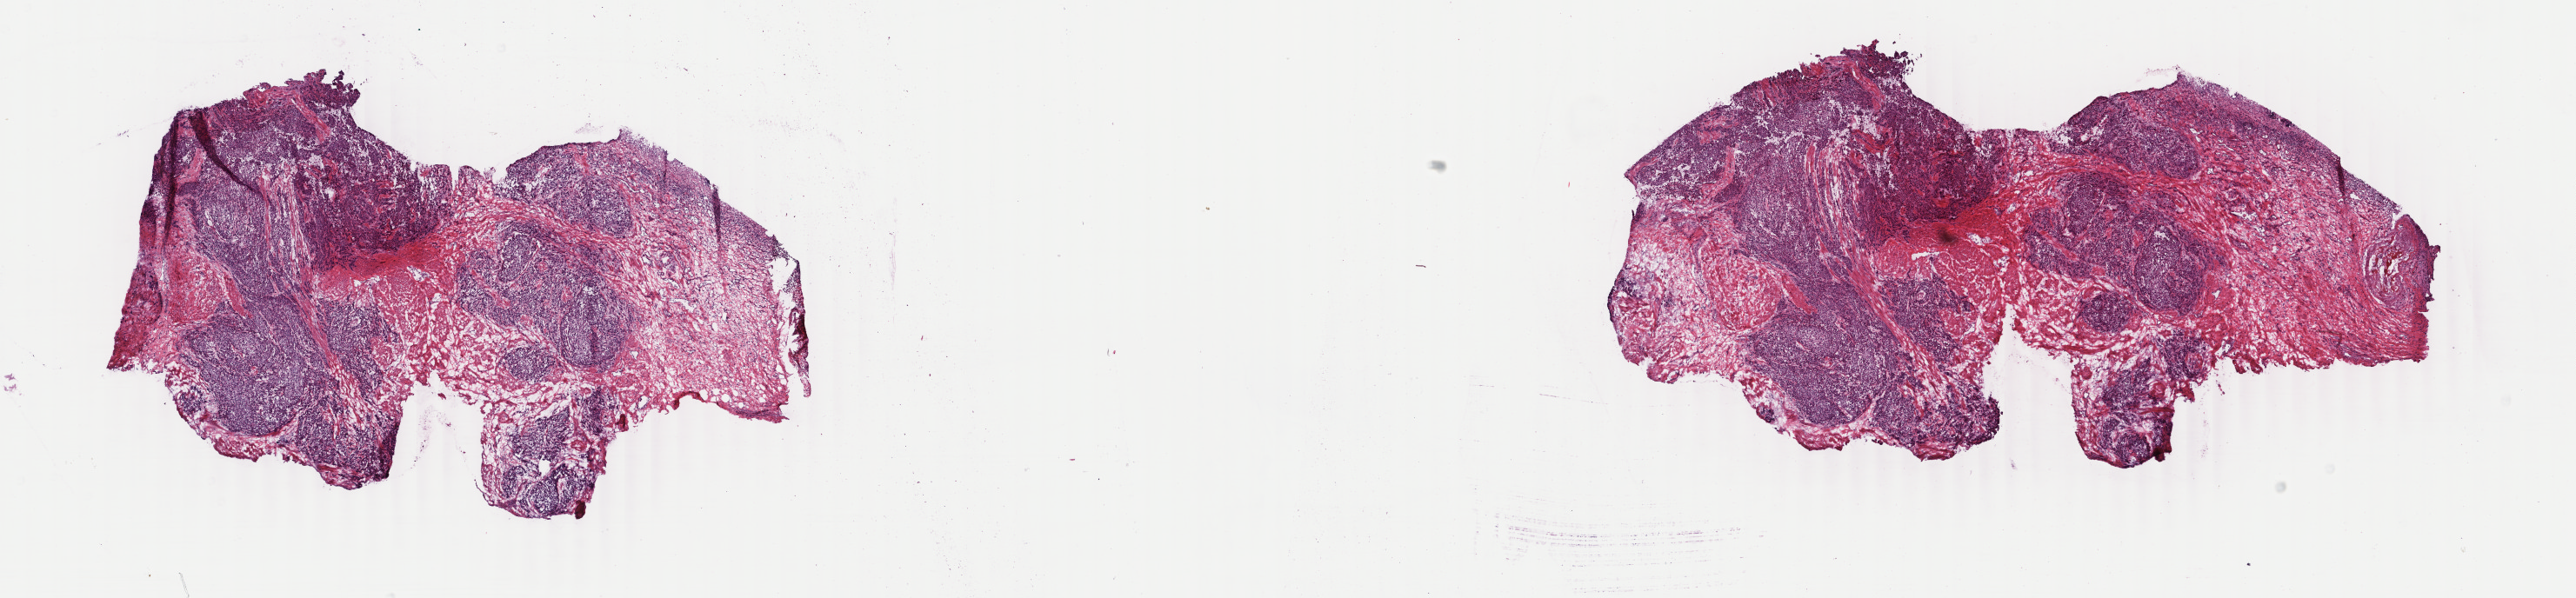
Digitized Hematoxylin and eosin (H&E) stained tissue section (whole slide) — whole scanned area (about 23.6 x 5.5 mm) shown as a low-resolution overview, frozen section from the top of the tissue portion, primary tumour sample from the bladder. Patient: male, age at initial diagnosis 77 years. Histologic grade: high grade. Slide review estimates, as recorded: tumour cells 48%, tumour nuclei 75%, normal cells 49%, stromal cells 2%, necrosis 1%. Inflammatory infiltration, as recorded: lymphocyte infiltration 4%, monocyte infiltration 0%, neutrophil infiltration 6%.
- AJCC pathologic stage: IV (6th edition)
- pathologic diagnosis: Transitional cell carcinoma